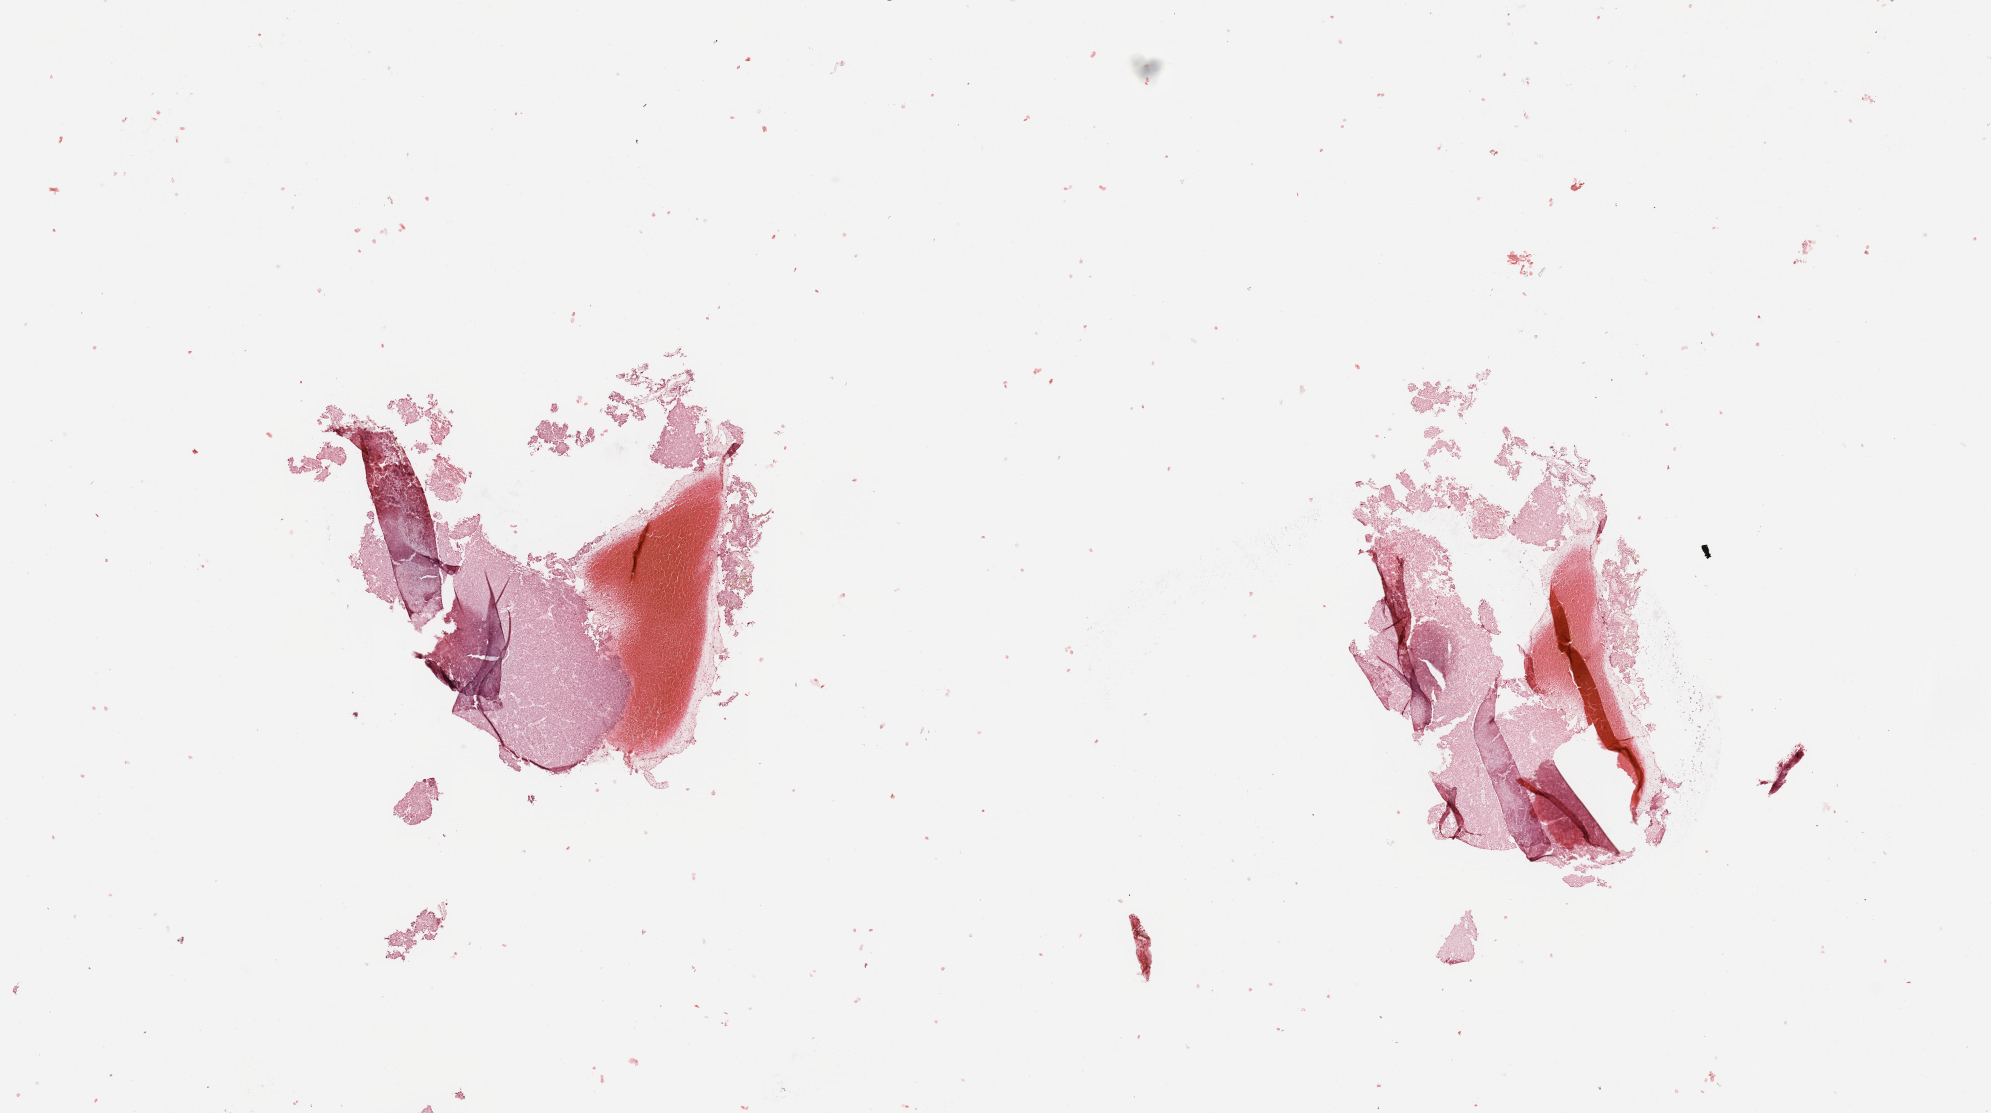
Whole-slide histology image, H&E — low-resolution overview of the scanned area, about 15.8 x 8.8 mm (from a 20x scan). Patient: female, age 59 years.
Primary tumour site (as recorded): gynecologic. Patient diagnosis (cohort enrolment): sarcoma (site not recorded at cohort level).